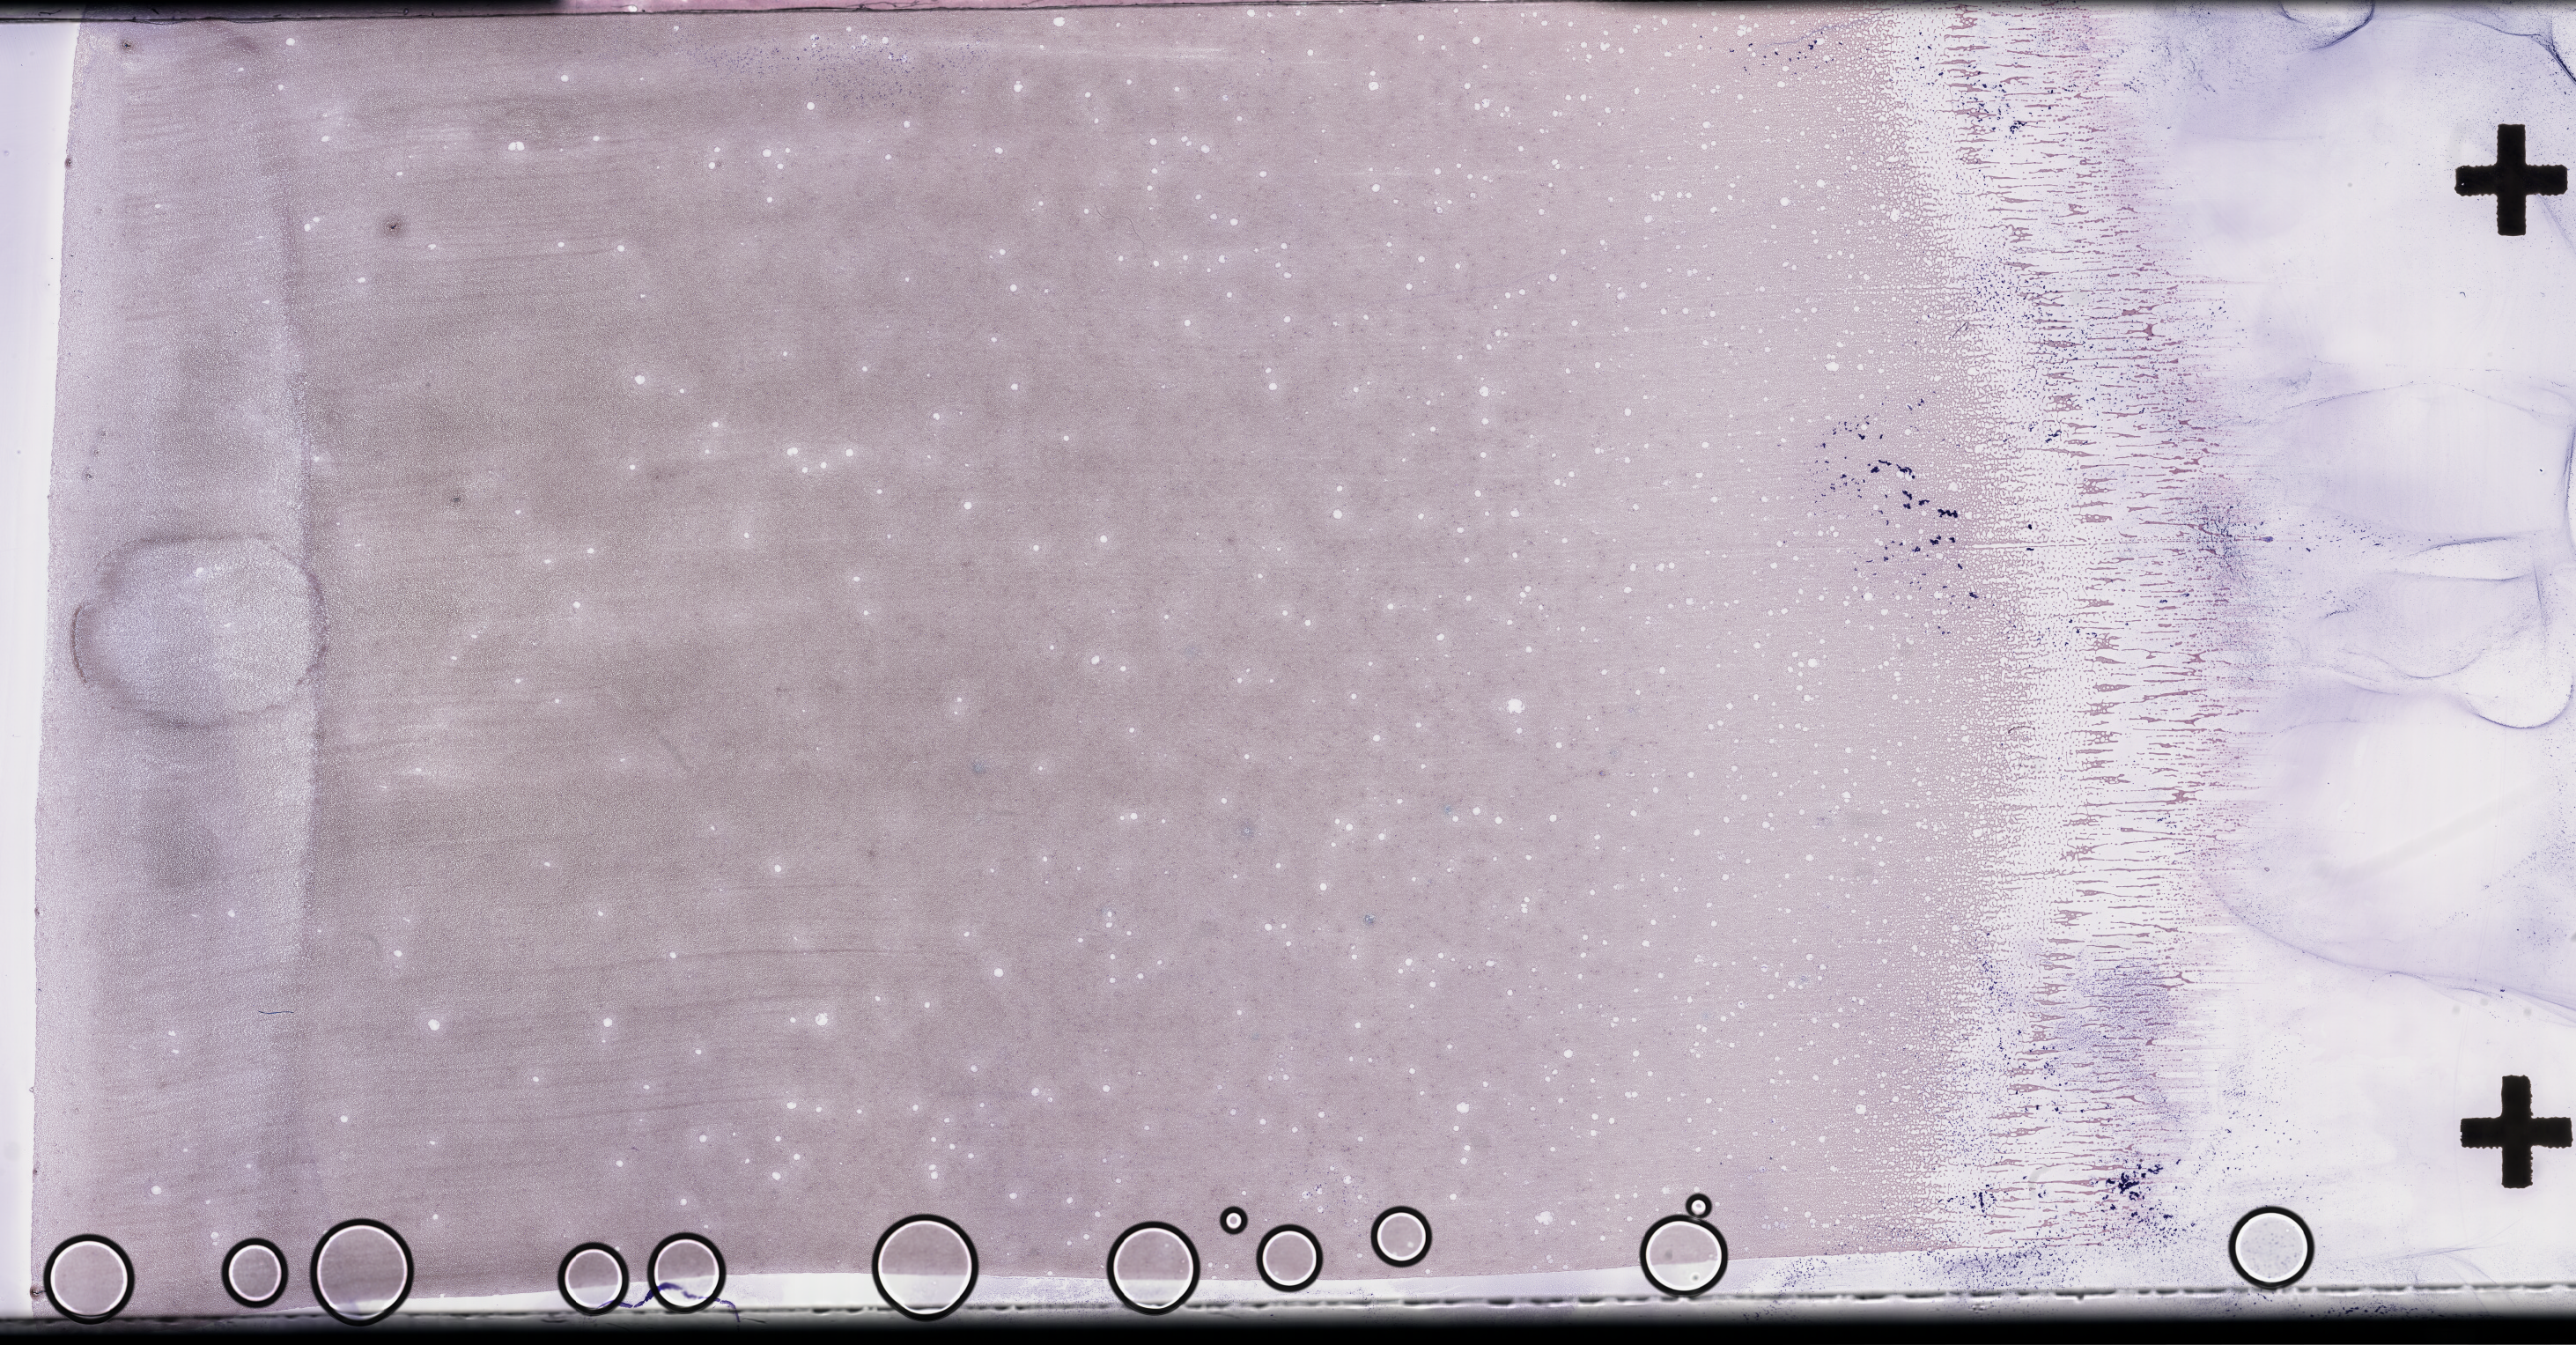
Whole-slide image of a whole blood smear, Wright–Giemsa stain, a low-resolution overview of the entire scanned area, about 47.2 x 24.7 mm. Collected on treatment. Patient: male.
Patient diagnosis: Plasma Cell Myeloma.